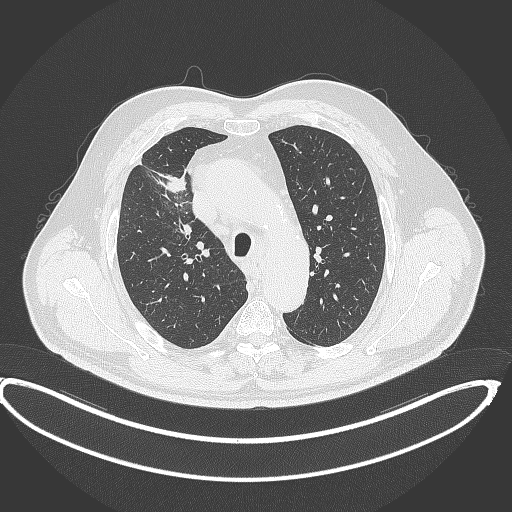
Chest CT, one axial slice; position 301 of 390 along the scan axis; lung window (W 1500 / L -600 HU); 1 mm slice thickness; 512 × 512 image matrix, field of view 448 × 448 mm. Patient: male, 62 years. From the clinical record (not read from this slice): clinical TNM (as recorded): T1c N3 M1c.
Structures marked on this image (rectangle marked by the reading radiologist):
- lung tumour (recorded histology: adenocarcinoma): bounding box (x1, y1, x2, y2) in pixels: (158, 173, 189, 194)